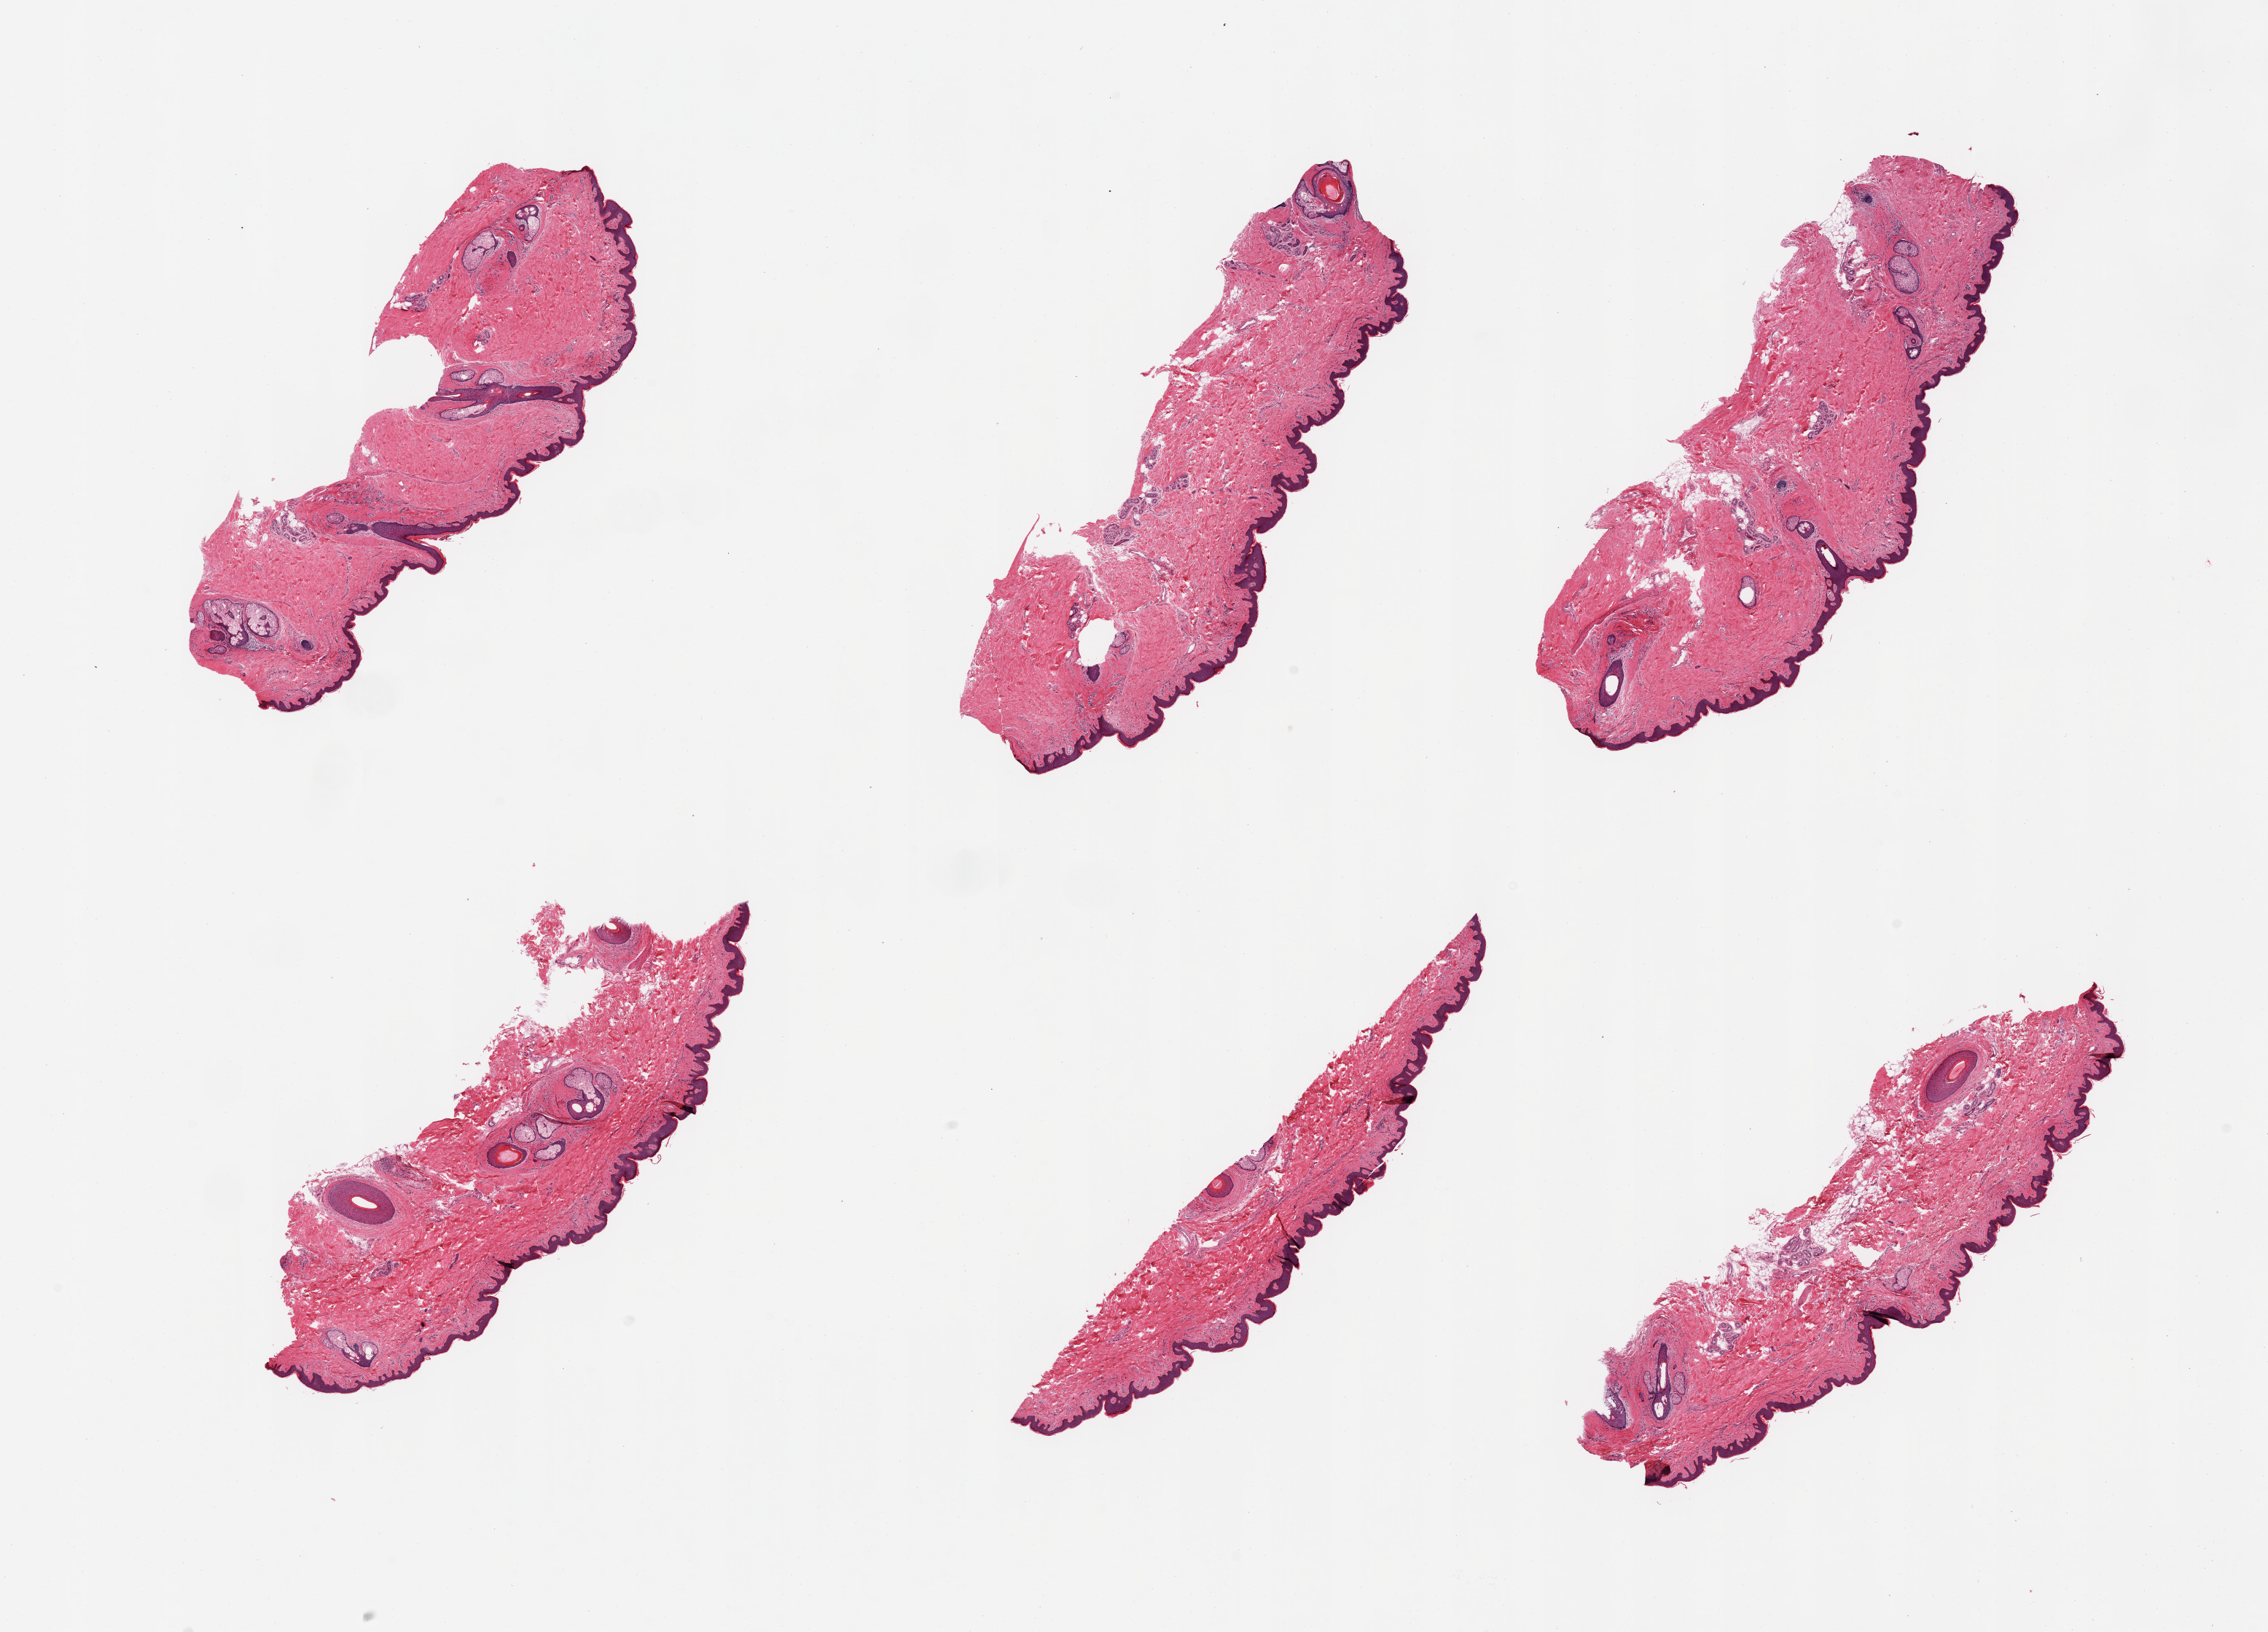
Whole-slide image, H&E stain, low-resolution overview of the scanned area, about 24.6 x 17.7 mm; PAXgene-fixed, paraffin-embedded tissue; section of skin of suprapubic region (target tissue); tissue donor sample. Donor: male.
* review note (as recorded): 6 pieces; hair-bearing skin with small amounts of periadnexal fat